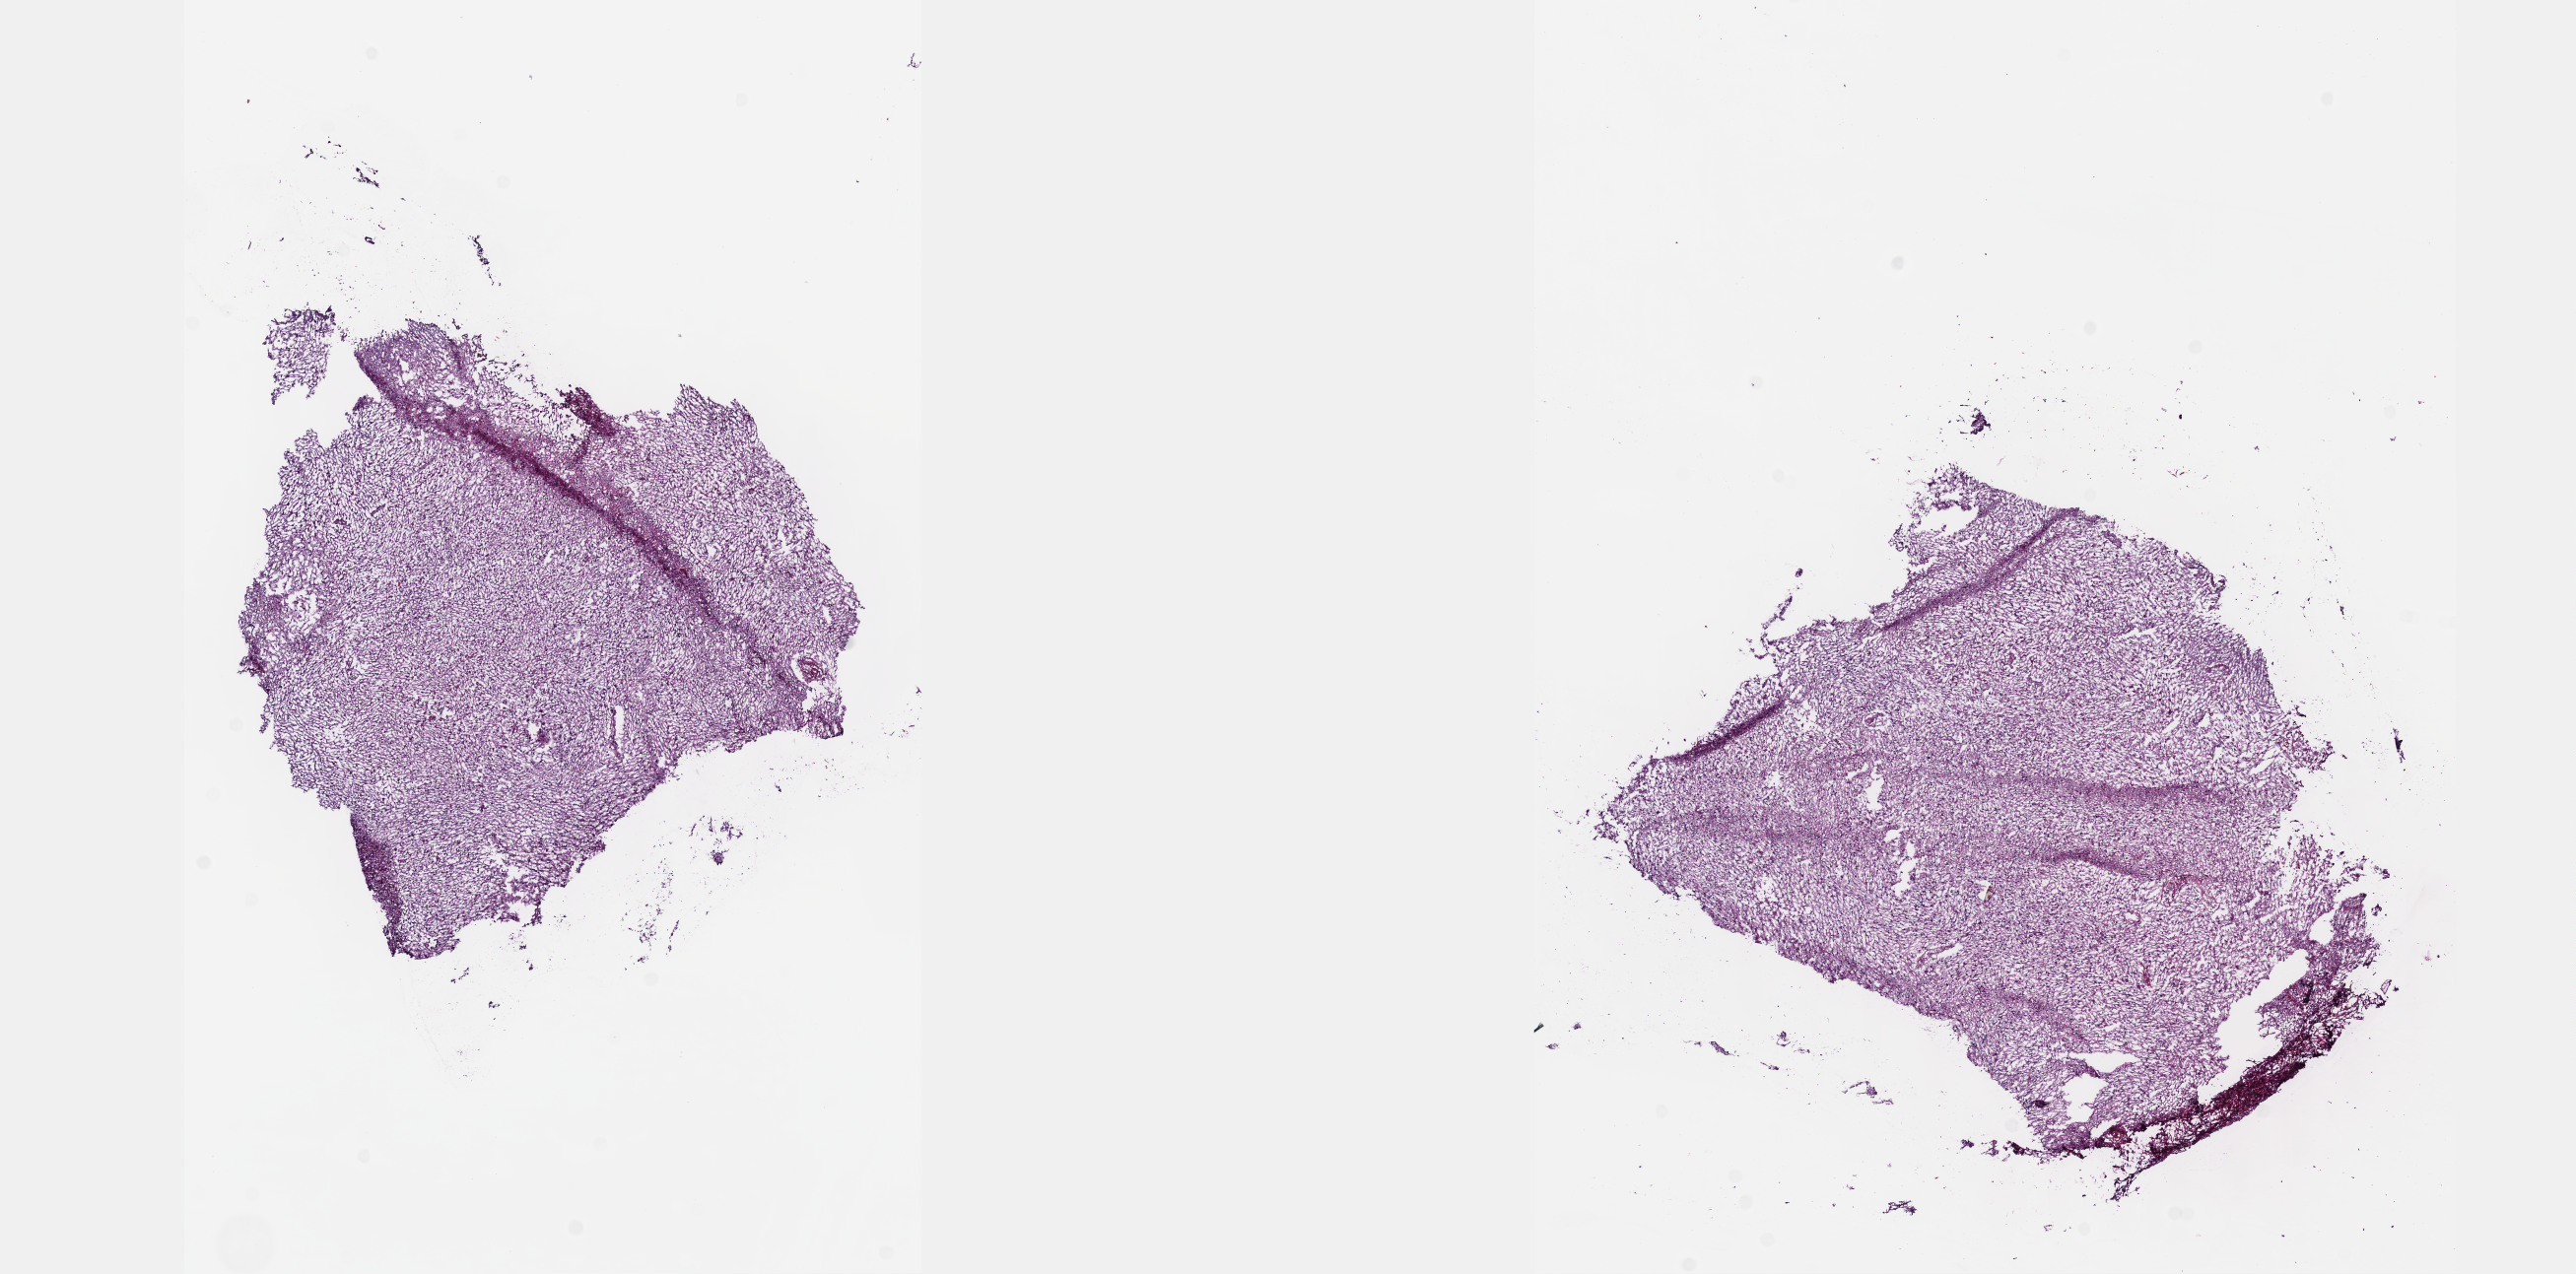
Whole-slide histology image, H&E, a low-resolution overview of the entire scanned area, about 21.1 x 10.4 mm, frozen section, sample: primary tumour, brain. Patient: male, age at initial diagnosis 46 years. Histologic grade: G3 (poorly differentiated). Slide review estimates, as recorded: tumour cells 60%, tumour nuclei 90%, normal cells 5%, stromal cells 35%, necrosis 0%. Infiltration values recorded for this section: lymphocyte infiltration 0%, monocyte infiltration 0%, neutrophil infiltration 0%.
Diagnosis: Astrocytoma, anaplastic (cerebrum).